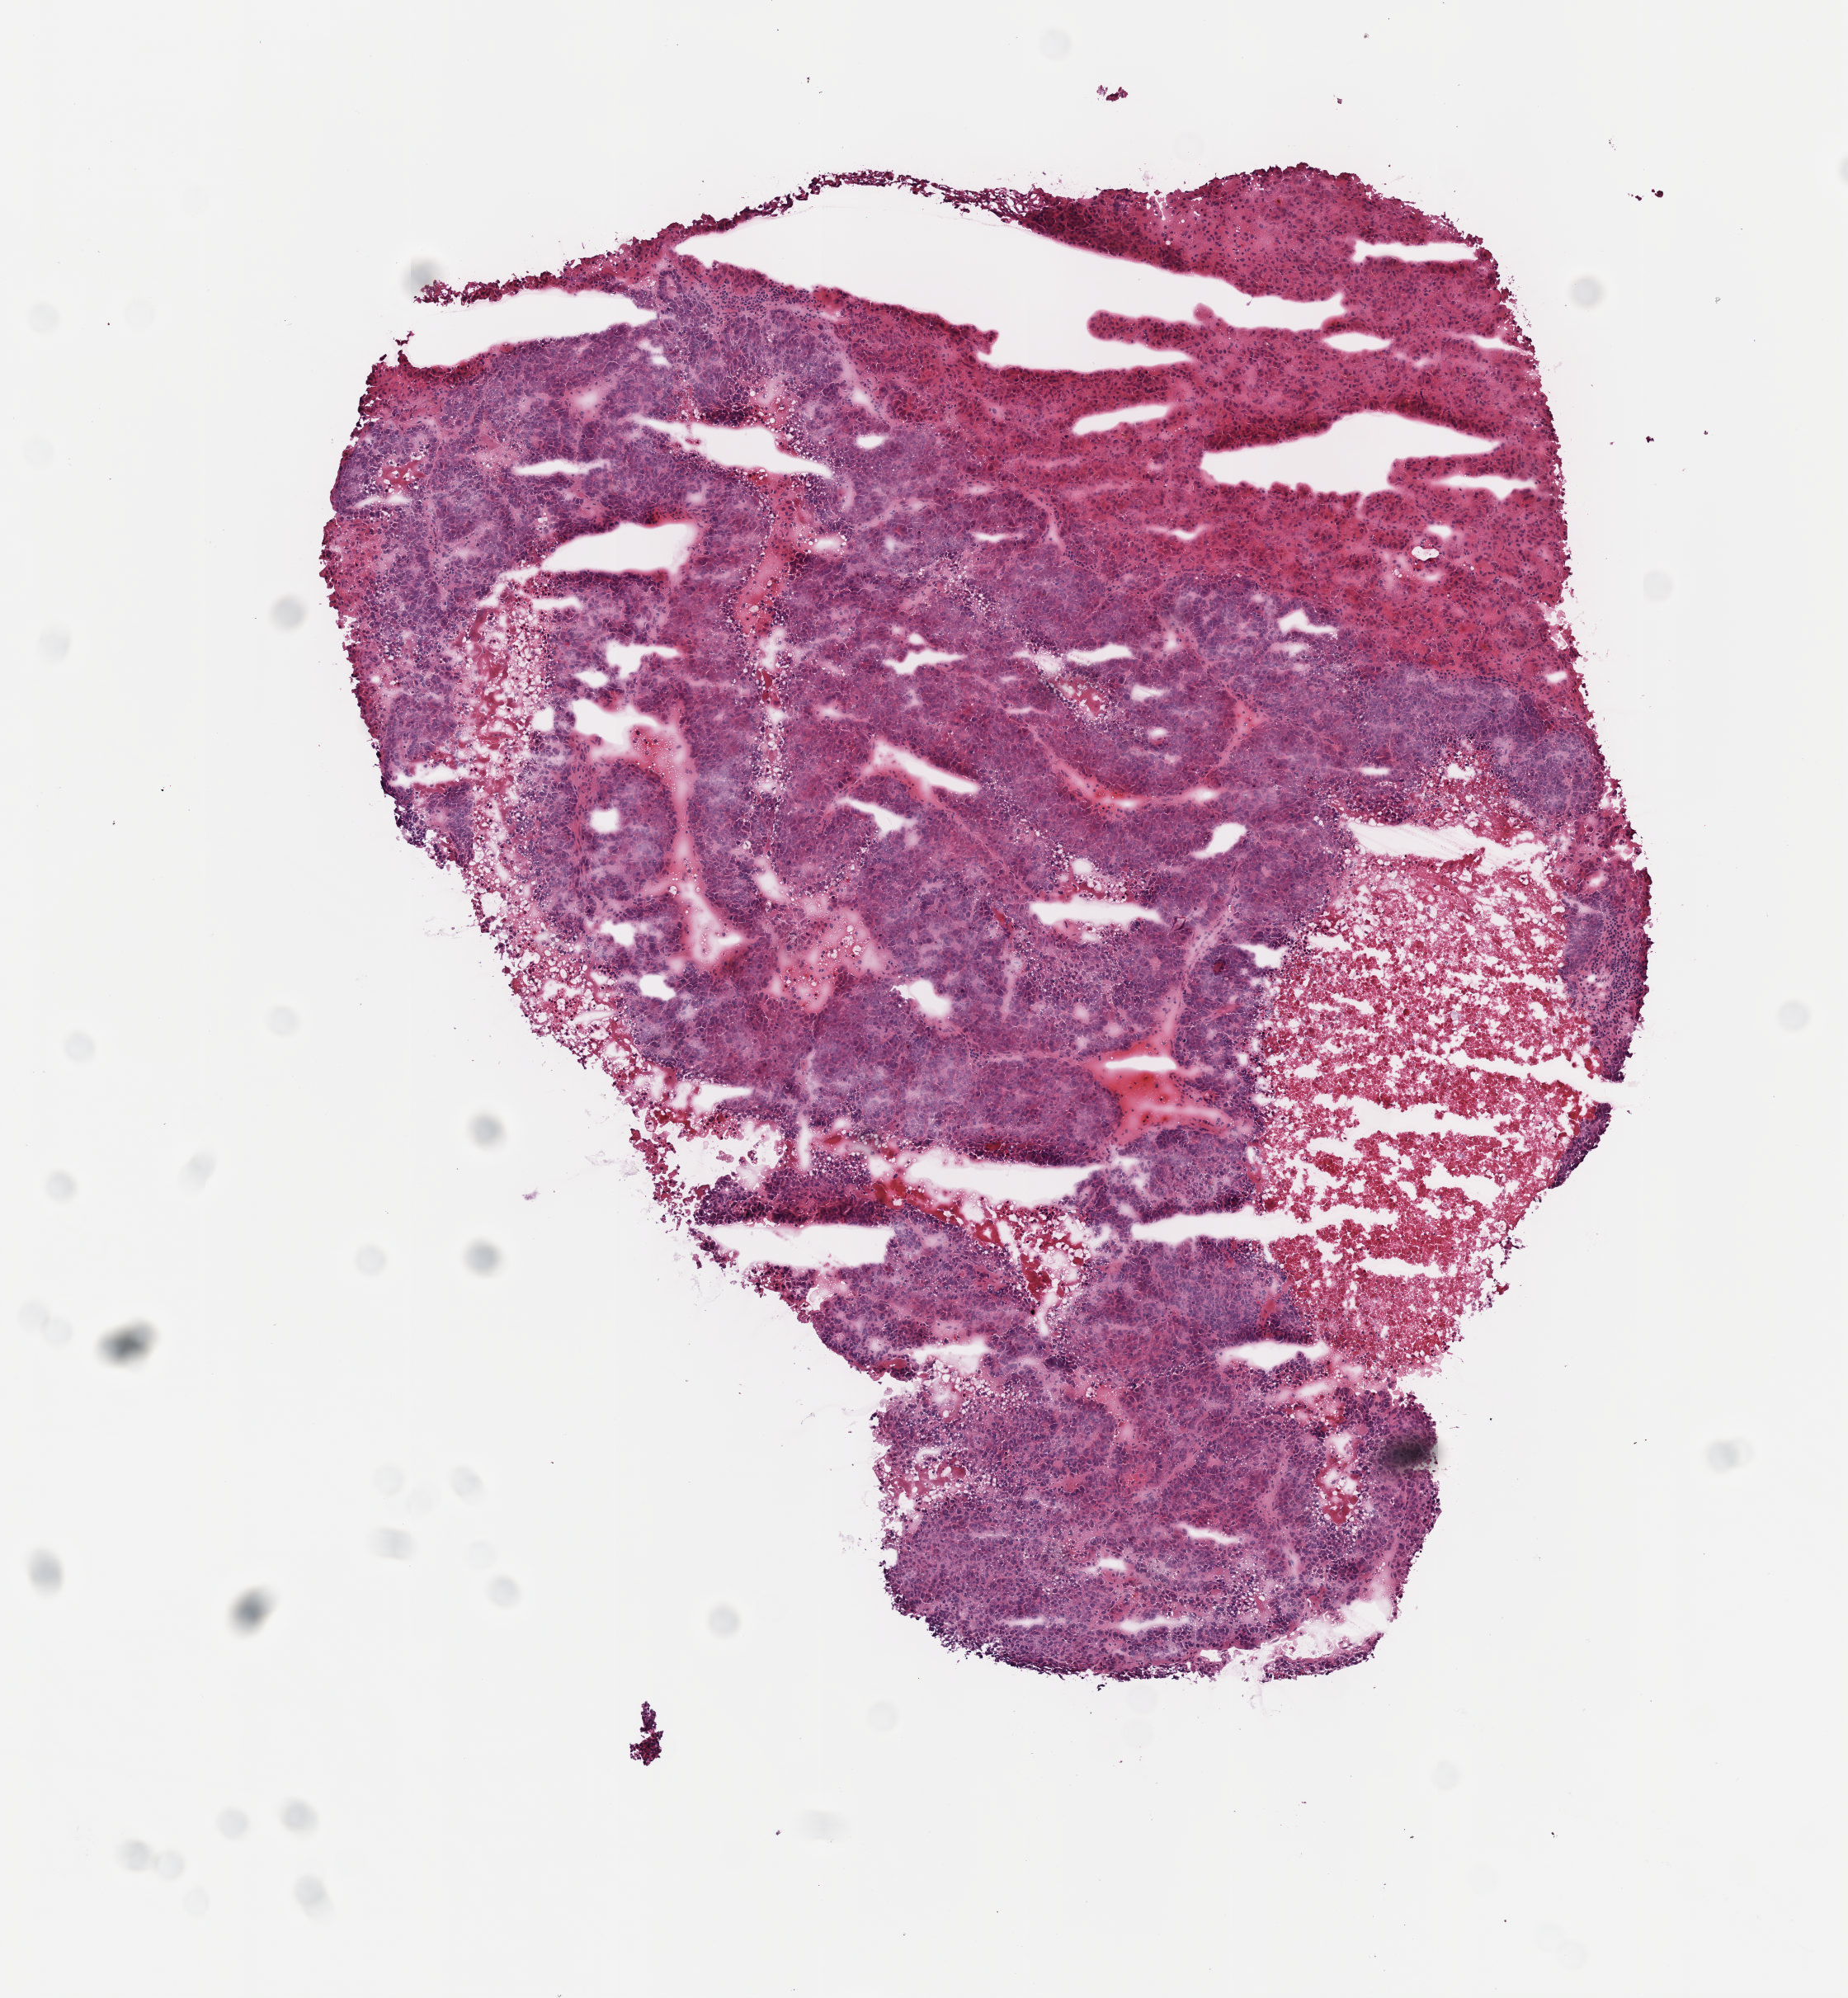
Digitized Hematoxylin and eosin (H&E) stained tissue section (whole slide), shown as a low-resolution overview of the whole scanned area (about 4.5 x 4.9 mm, slide scanned at 40x), frozen section from the top of the tissue portion, sample: primary tumour, liver. Patient: male, age at initial diagnosis 64 years. Histologic grade: G3 (poorly differentiated). Composition of this section per pathologist review: tumour cells 70%, tumour nuclei 80%, normal cells 20%, stromal cells 0%, necrosis 10%. Inflammatory infiltration, as recorded: lymphocyte infiltration 0%, monocyte infiltration 0%, neutrophil infiltration 0%.
• AJCC pathologic stage: I
• histologic diagnosis: Hepatocellular carcinoma, NOS